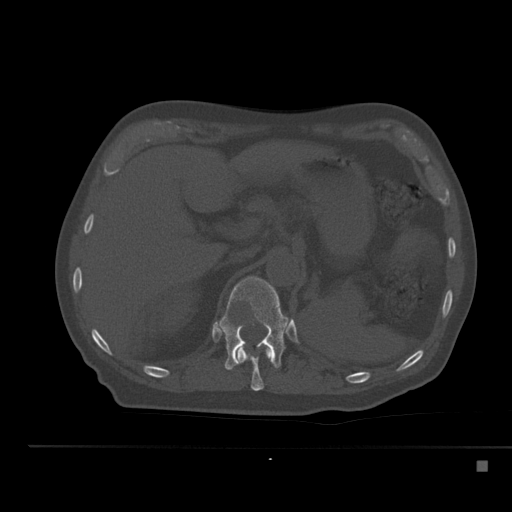
CT including the spine, one axial slice; position 234 of 517 along the scan axis; reconstruction kernel Br40s; 120 kVp; bone window (W 1800 / L 400 HU); 1.5 mm slice thickness; 512 × 512 image matrix, field of view 408 × 408 mm. Male patient, age 70 years. From the clinical record (not read from this slice): primary cancer: renal; vertebrae with lytic lesions (as recorded): T4, T6, T10, T12, L3, L4, L5.
Structures marked on this image (semi-automatically segmented with operator editing):
- T11 vertebra: bounding box (x1, y1, x2, y2) in pixels: (235, 345, 273, 391)
- T12 vertebra: (217, 276, 290, 370)